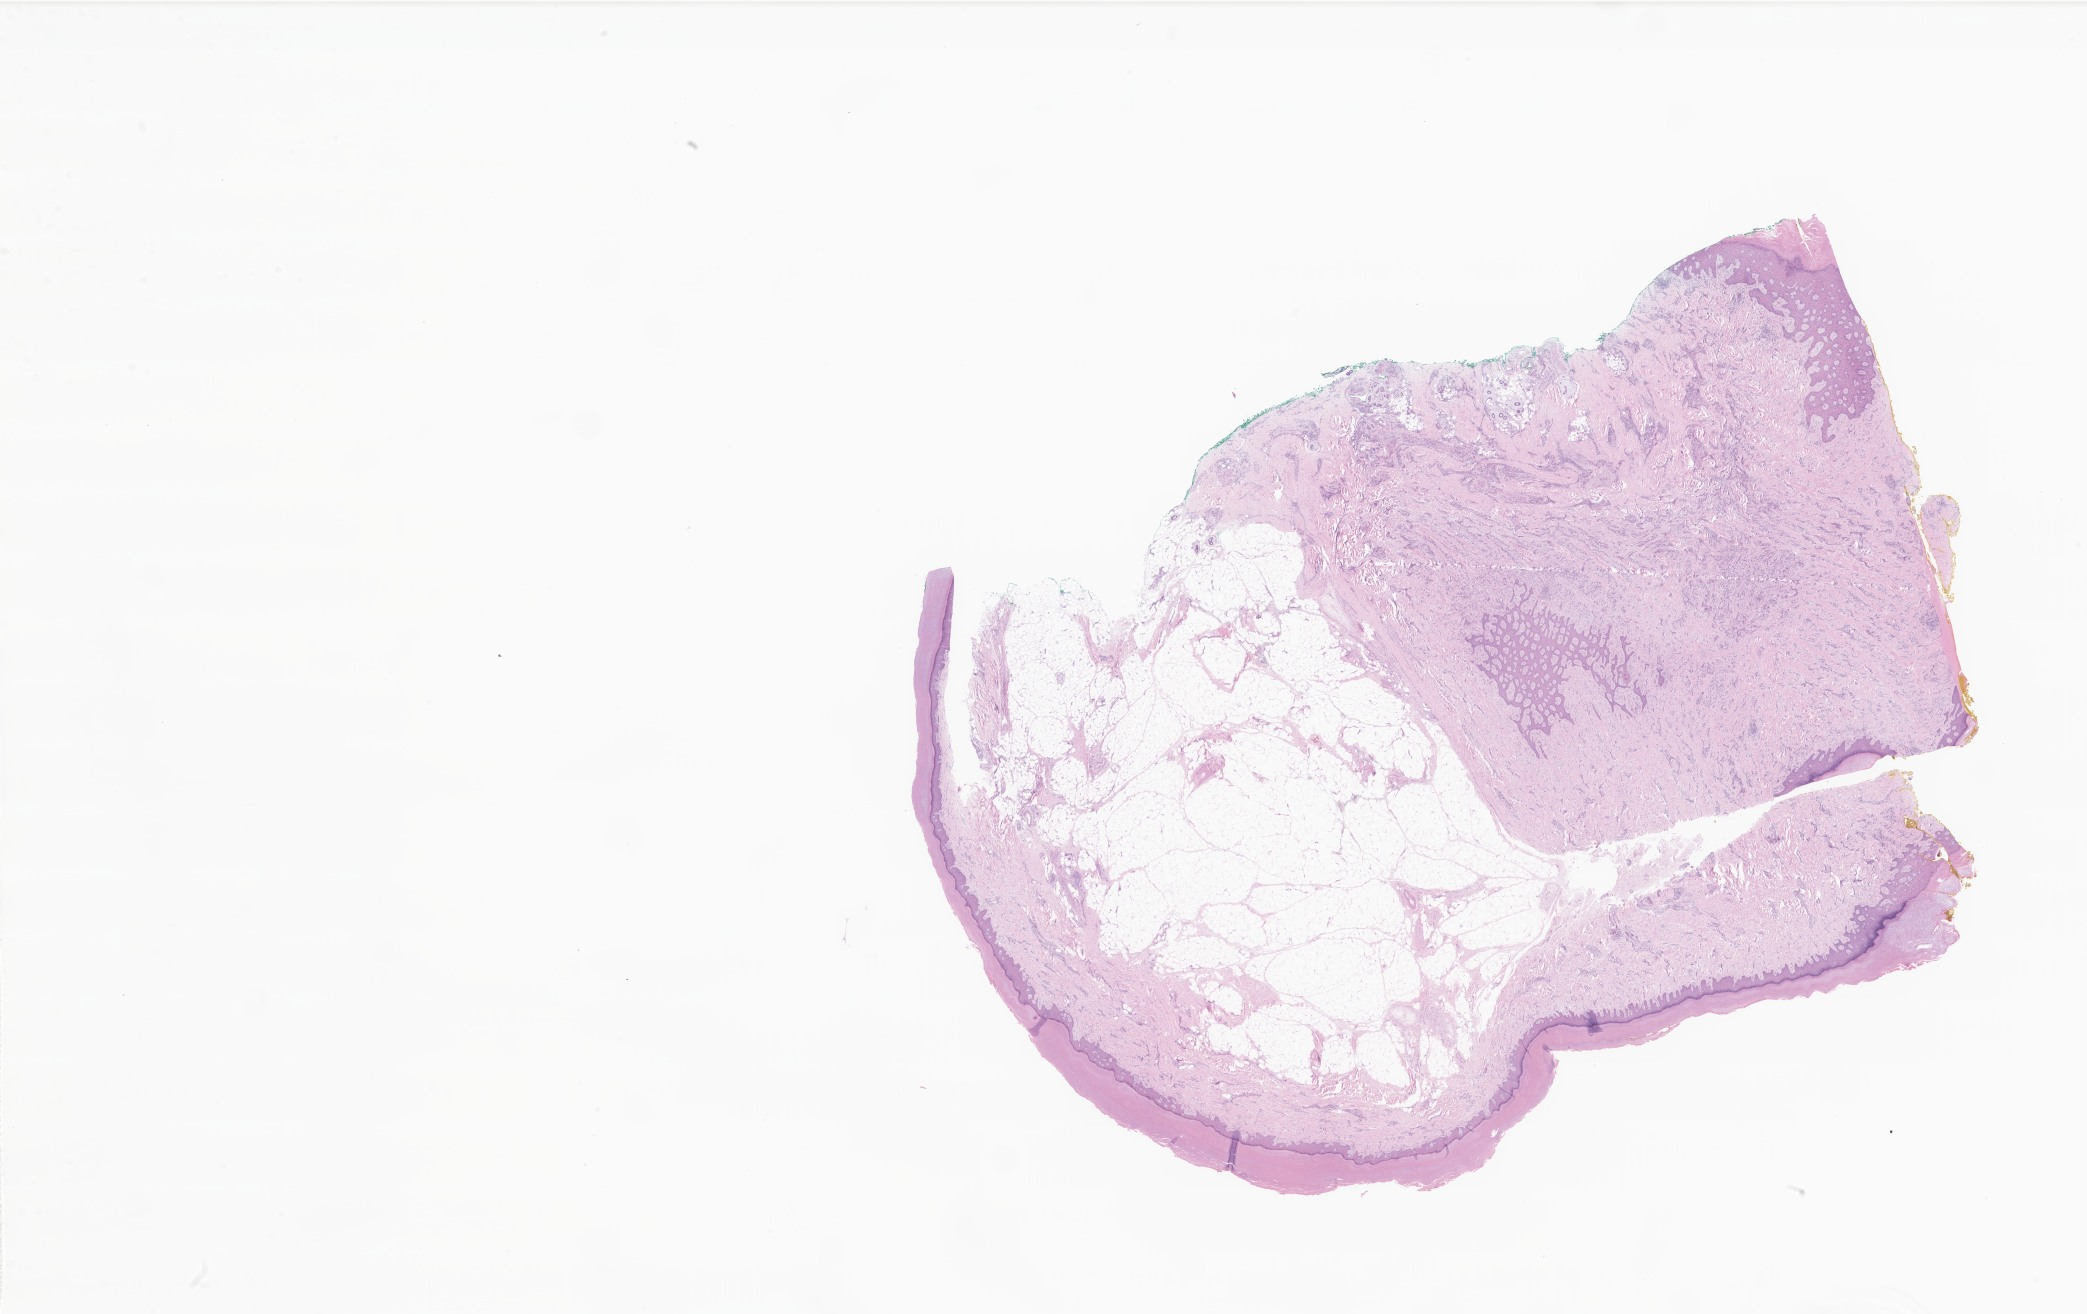
Digitized haematoxylin and eosin-stained section of tumor tissue from the skin of upper limb — shown as a low-resolution overview of the whole scanned area (about 35.2 x 22.2 mm); formalin-fixed paraffin-embedded section. Patient female; age 292 months (24 years 4 months).
Recorded diagnosis: Squamous cell carcinoma, NOS.